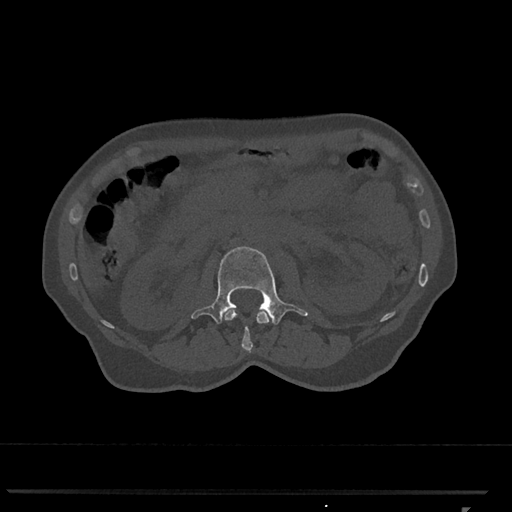
CT including the spine, one axial slice; position 356 of 793 along the scan axis; reconstruction kernel Br40s/3; 120 kVp; bone window (W 1800 / L 400 HU); 0.5 mm slice thickness; 512 × 512 image matrix. Female patient, age 62 years. From the clinical record (not read from this slice): primary cancer: renal.
Outlined on this slice (semi-automatic segmentation, software-assisted and operator-edited):
- L1 vertebra: box from (x=224, y=309) to (x=270, y=352) px
- L2 vertebra: (x=191, y=246)–(x=308, y=325)